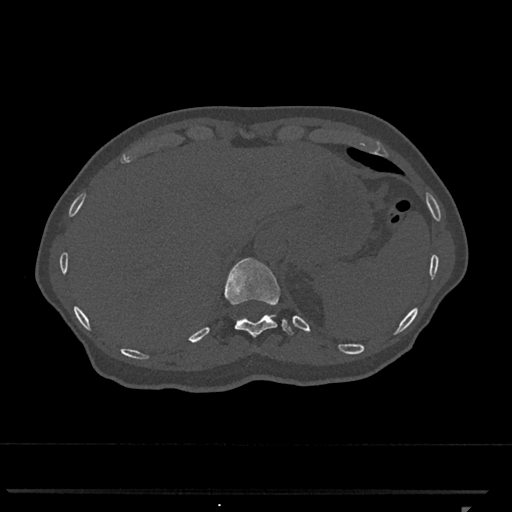
CT including the spine, one axial slice; position 513 of 793 along the scan axis; reconstruction kernel Br40s/3; 120 kVp; bone window (W 1800 / L 400 HU); 0.5 mm slice thickness; 512 × 512 image matrix. Patient: female, 62 years. From the clinical record (not read from this slice): primary cancer: renal.
Structures marked on this image (semi-automatically segmented with operator editing):
- T11 vertebra: box from (x=225, y=258) to (x=293, y=338) px